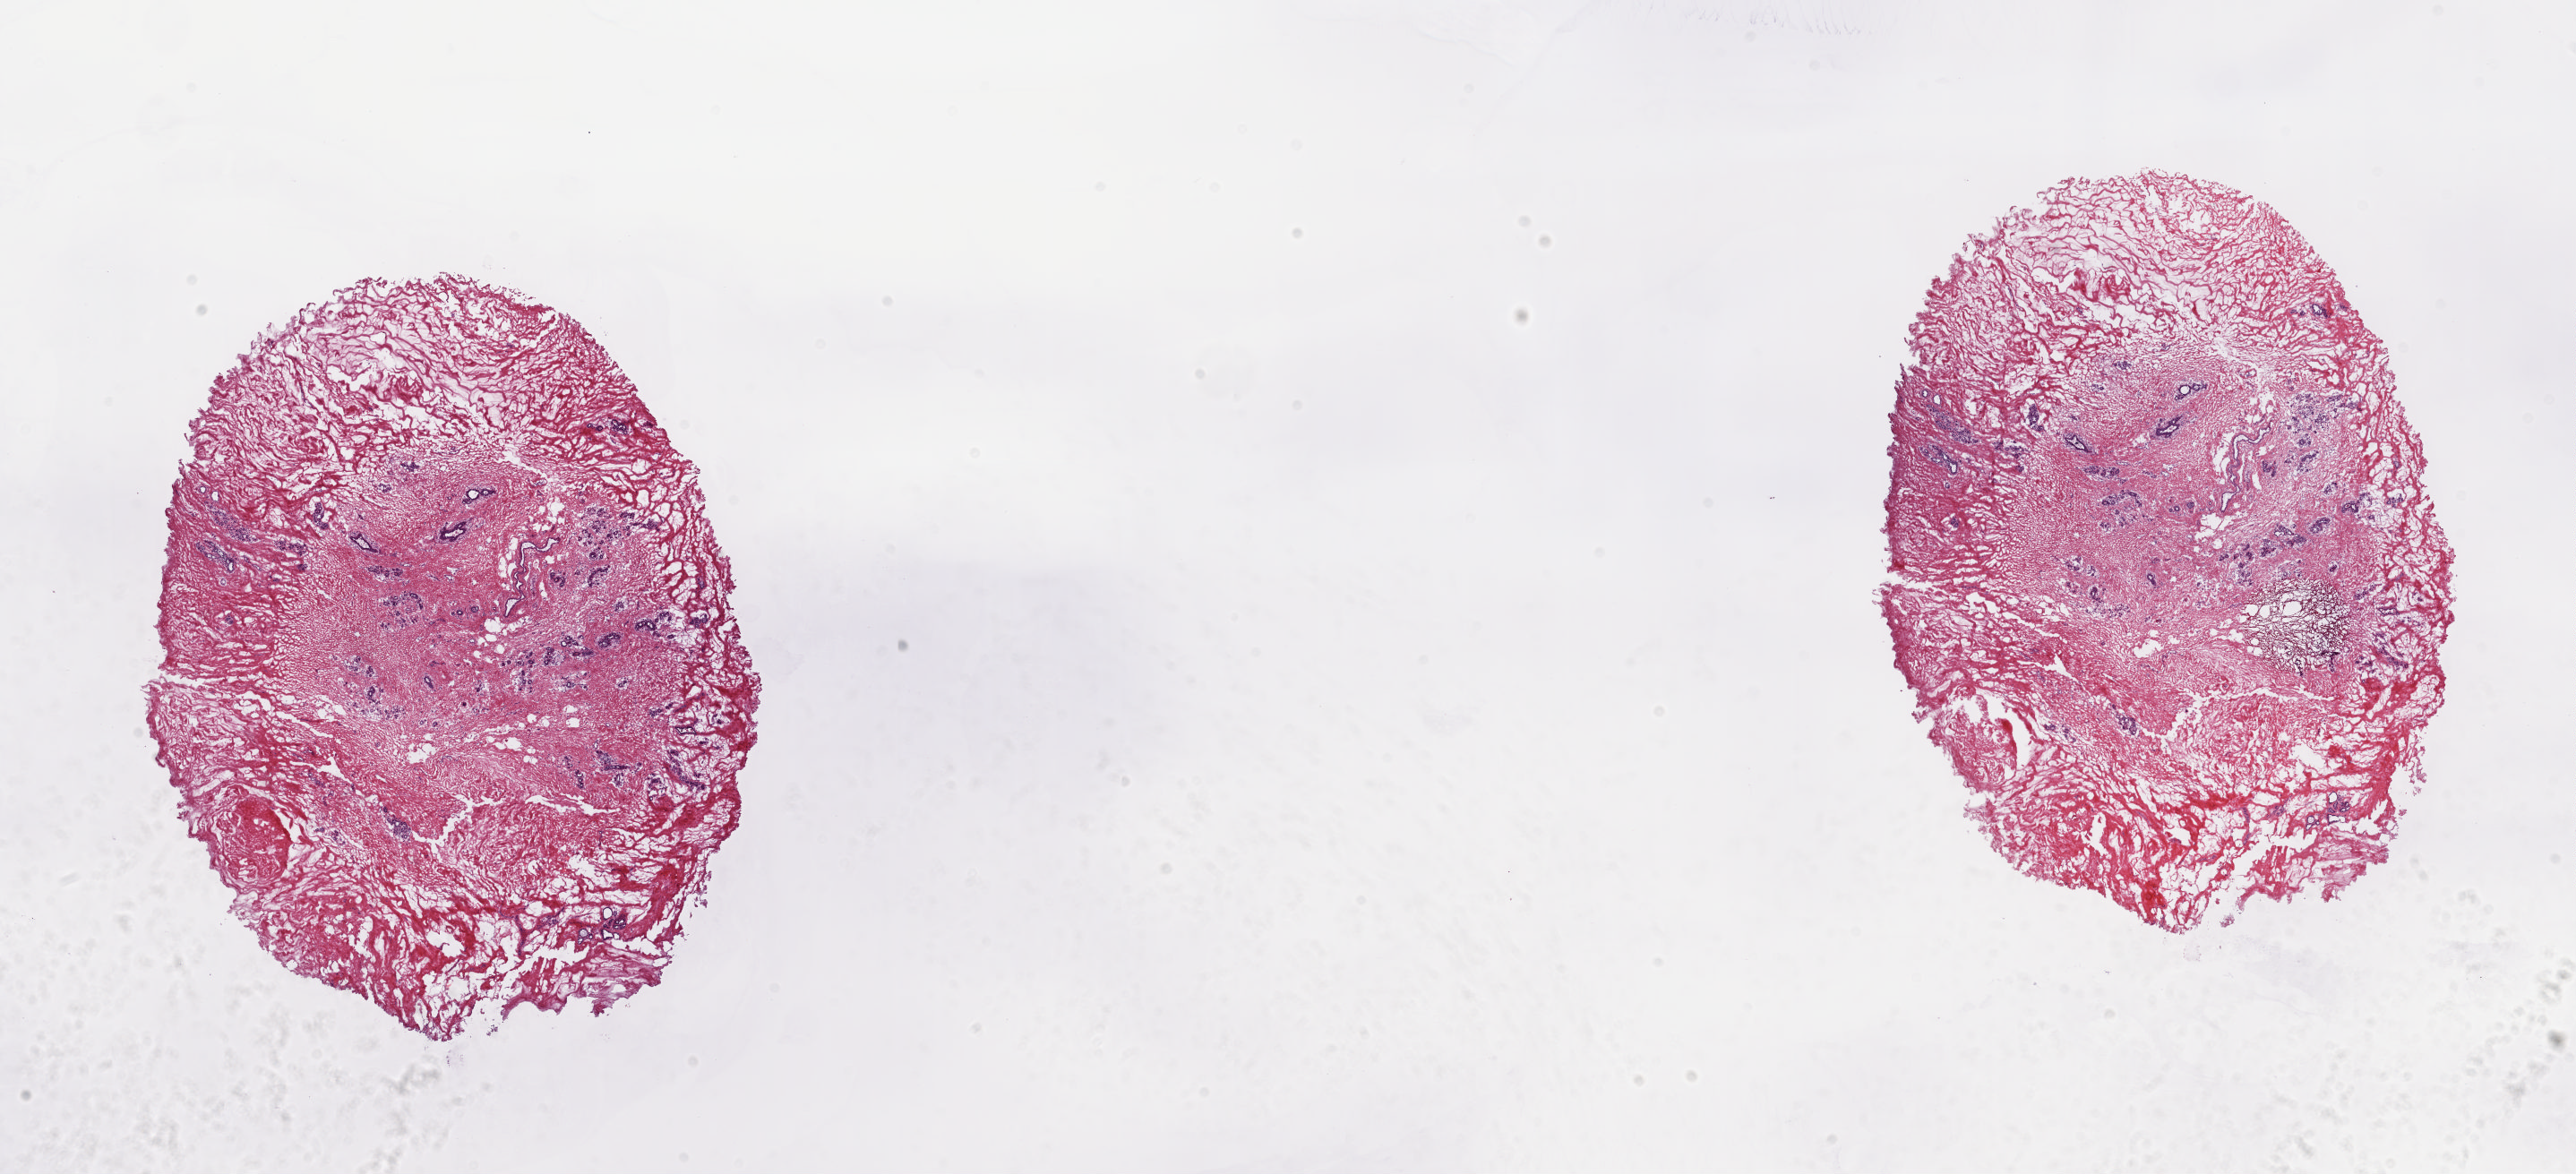
Digitized H&E-stained tissue section (whole slide), shown as a low-resolution overview of the whole scanned area (about 22.8 x 10.4 mm, from a 20x scan), frozen section from the top of the tissue portion, solid tissue normal (non-tumour tissue) sample from the breast. Female patient; age at initial diagnosis 40 years. Slide review estimates, as recorded: tumour cells 0%, tumour nuclei 0%.
This section: solid tissue normal sample (biorepository sample class). Patient diagnosis: Lobular carcinoma, NOS.